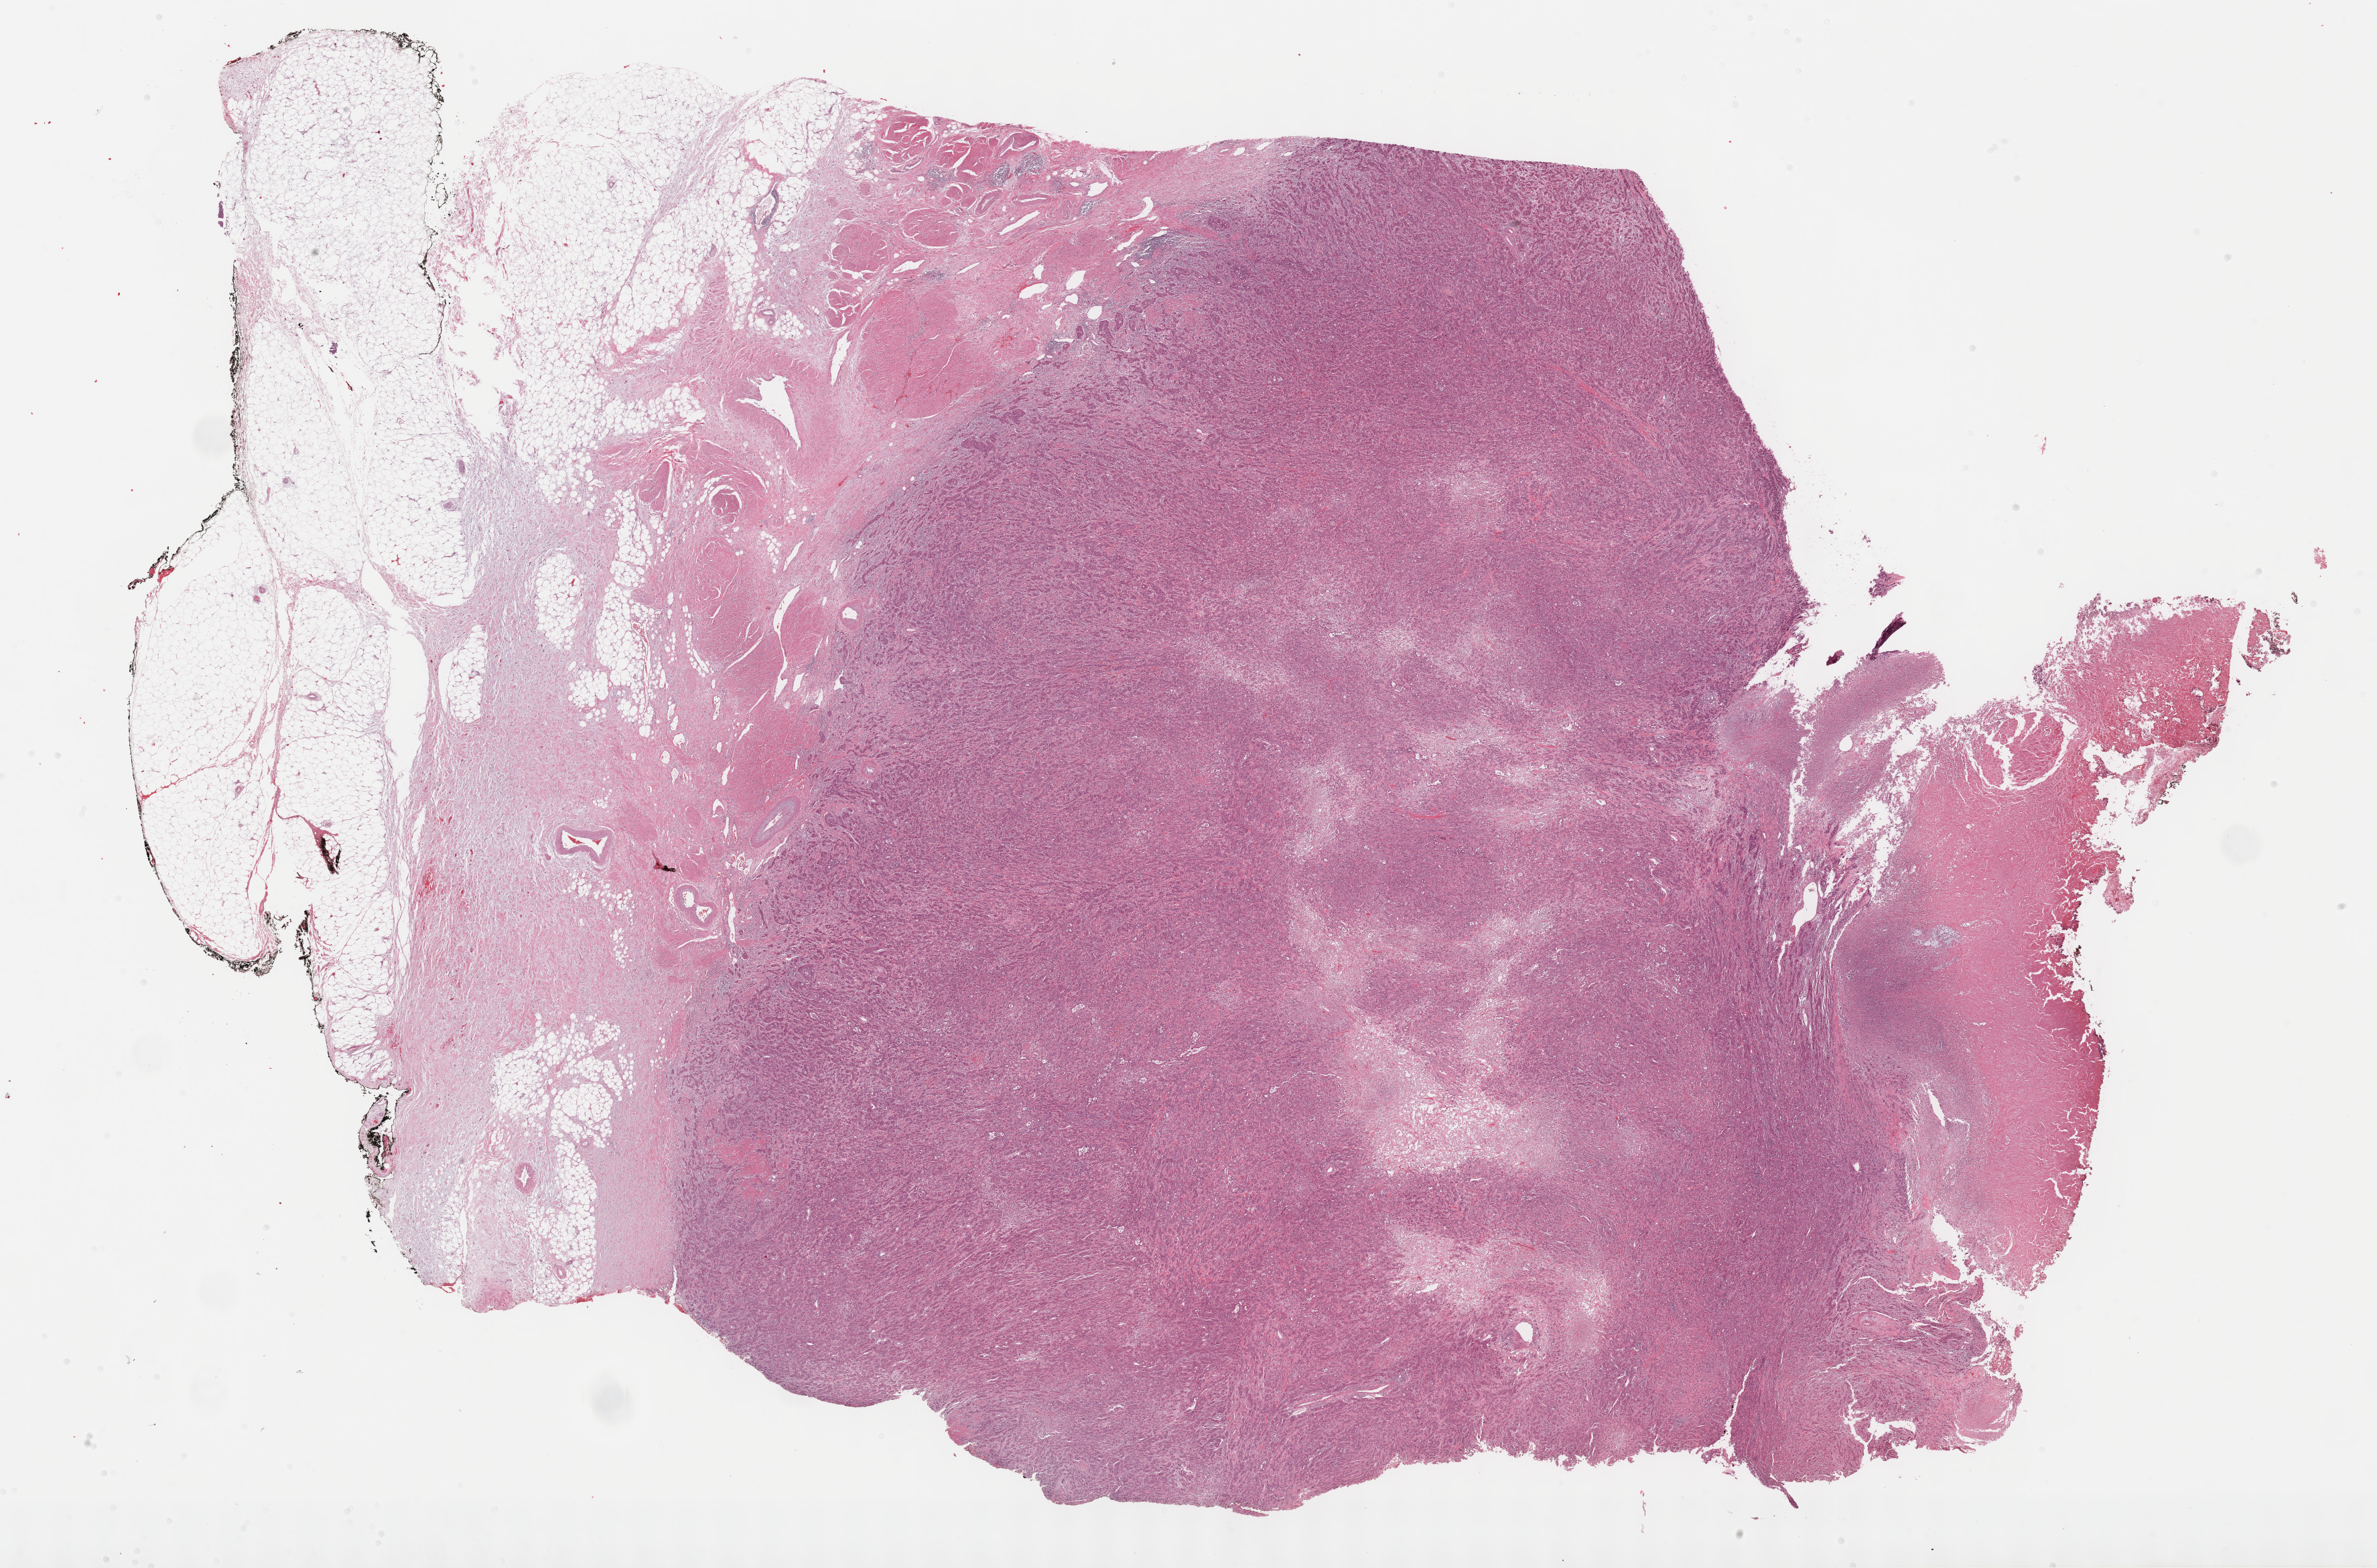
Digitized H&E-stained tissue section (whole slide) — shown as a low-resolution overview of the whole scanned area (about 28.7 x 18.9 mm), formalin-fixed paraffin-embedded (FFPE) diagnostic section, sample: primary tumour, bladder. Male patient; age at initial diagnosis 77 years. Histologic grade: high grade.
AJCC pathologic stage: III (6th edition). Diagnosis: Transitional cell carcinoma.